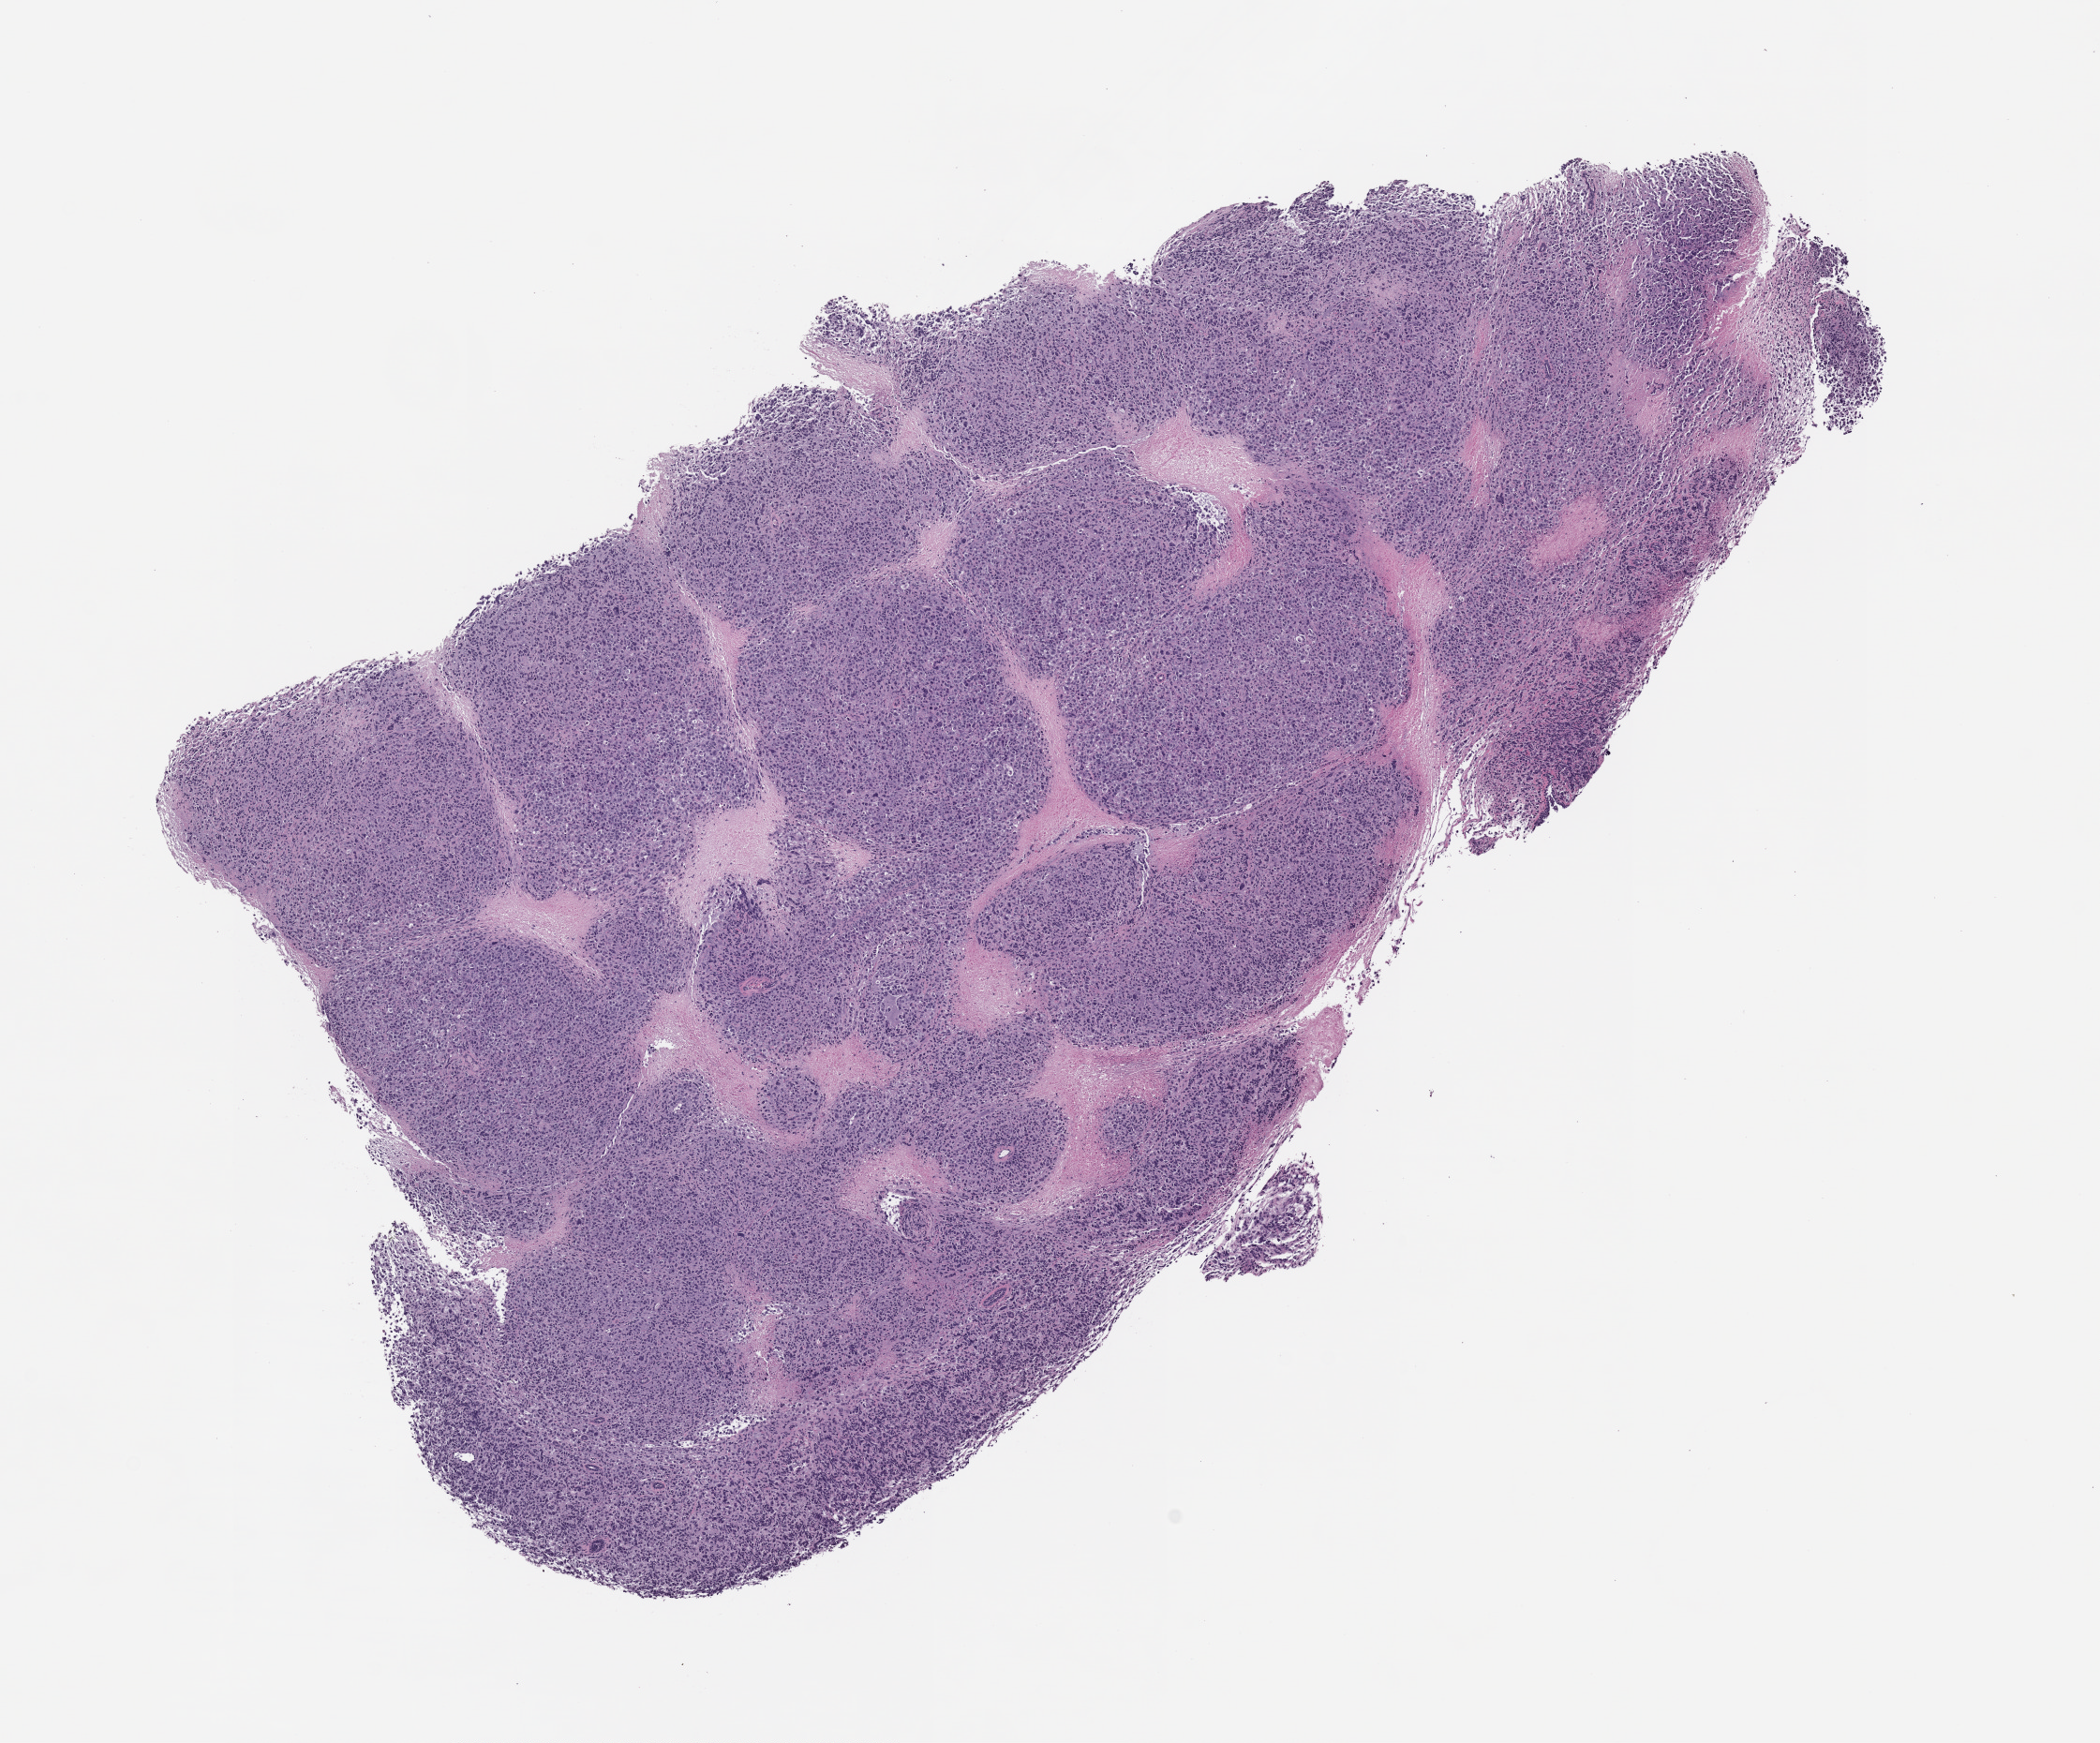
Whole-slide image, hematoxylin and eosin (H&E): patient-derived xenograft (human tumor grown in a mouse), a low-resolution overview of the entire scanned area, about 9.0 x 7.5 mm.
• specimen: FFPE section